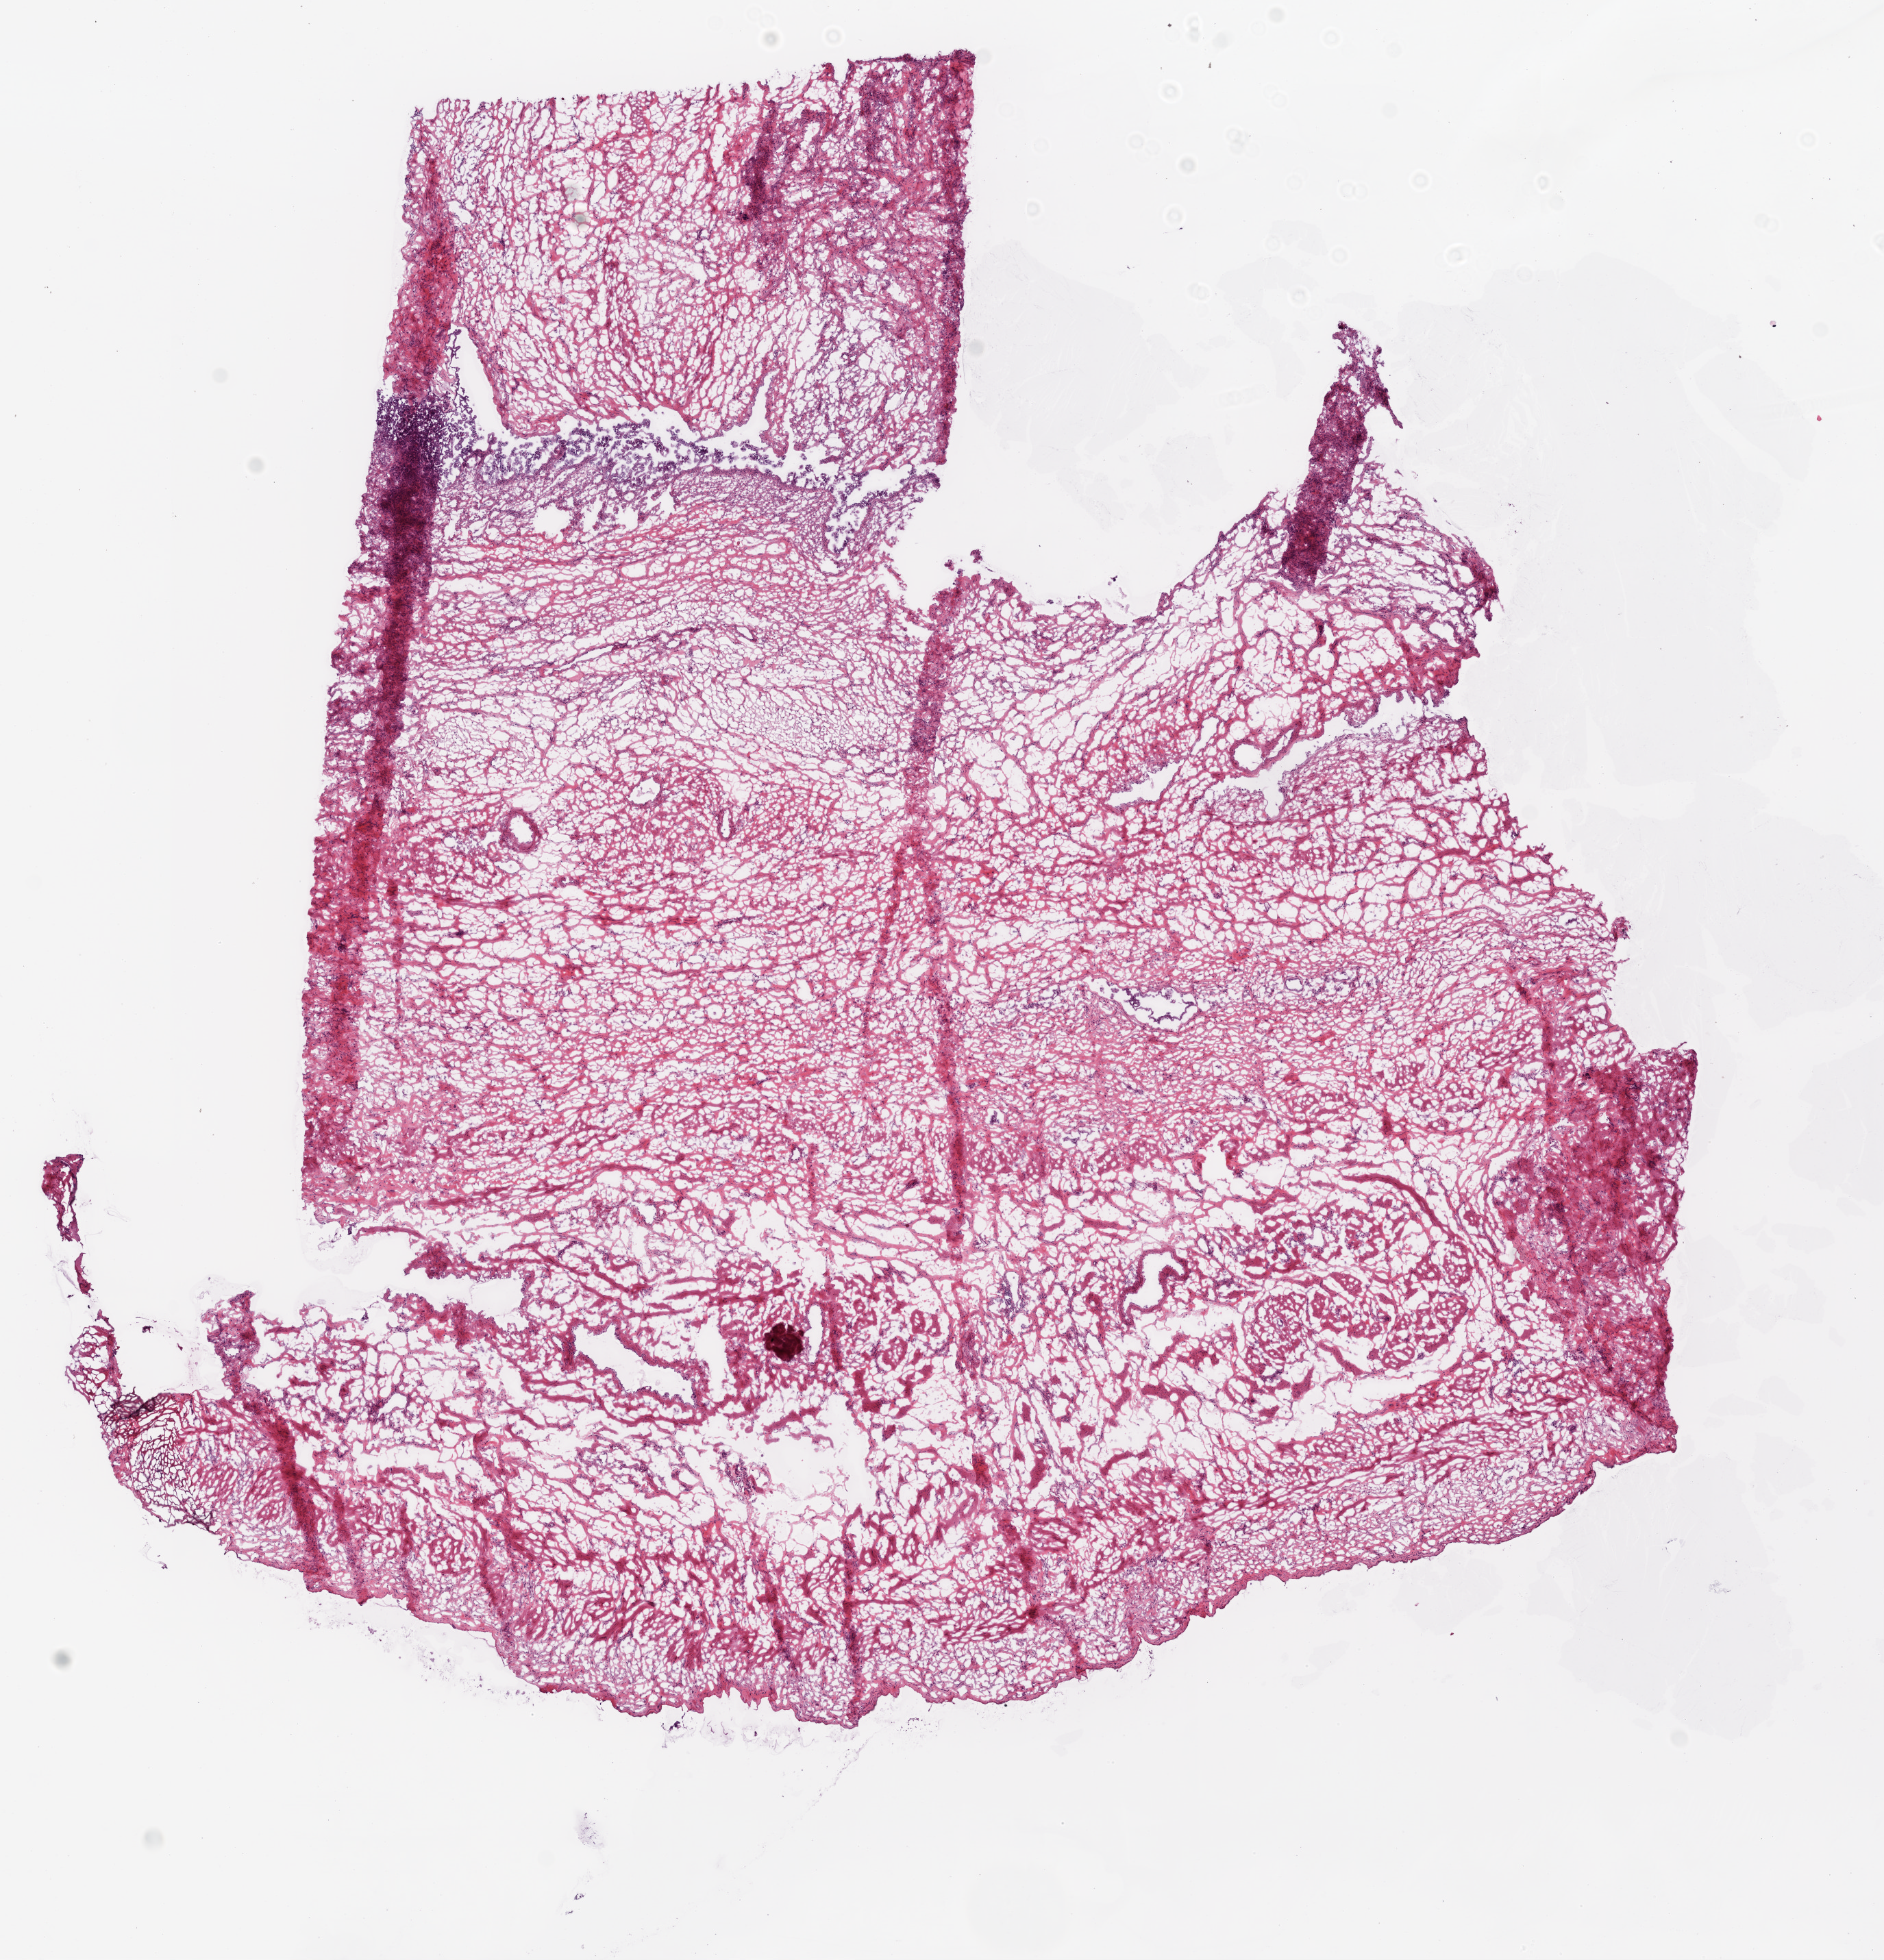
H&E whole-slide image — shown as a low-resolution overview of the whole scanned area (about 11.0 x 11.5 mm, from a 20x scan). Frozen section from the bottom of the tissue portion. Sample: solid tissue normal (non-tumour tissue), ovary. Female patient; age at initial diagnosis 56 years.
• this section: solid tissue normal sample (biorepository sample class)
• patient diagnosis: Serous cystadenocarcinoma, NOS